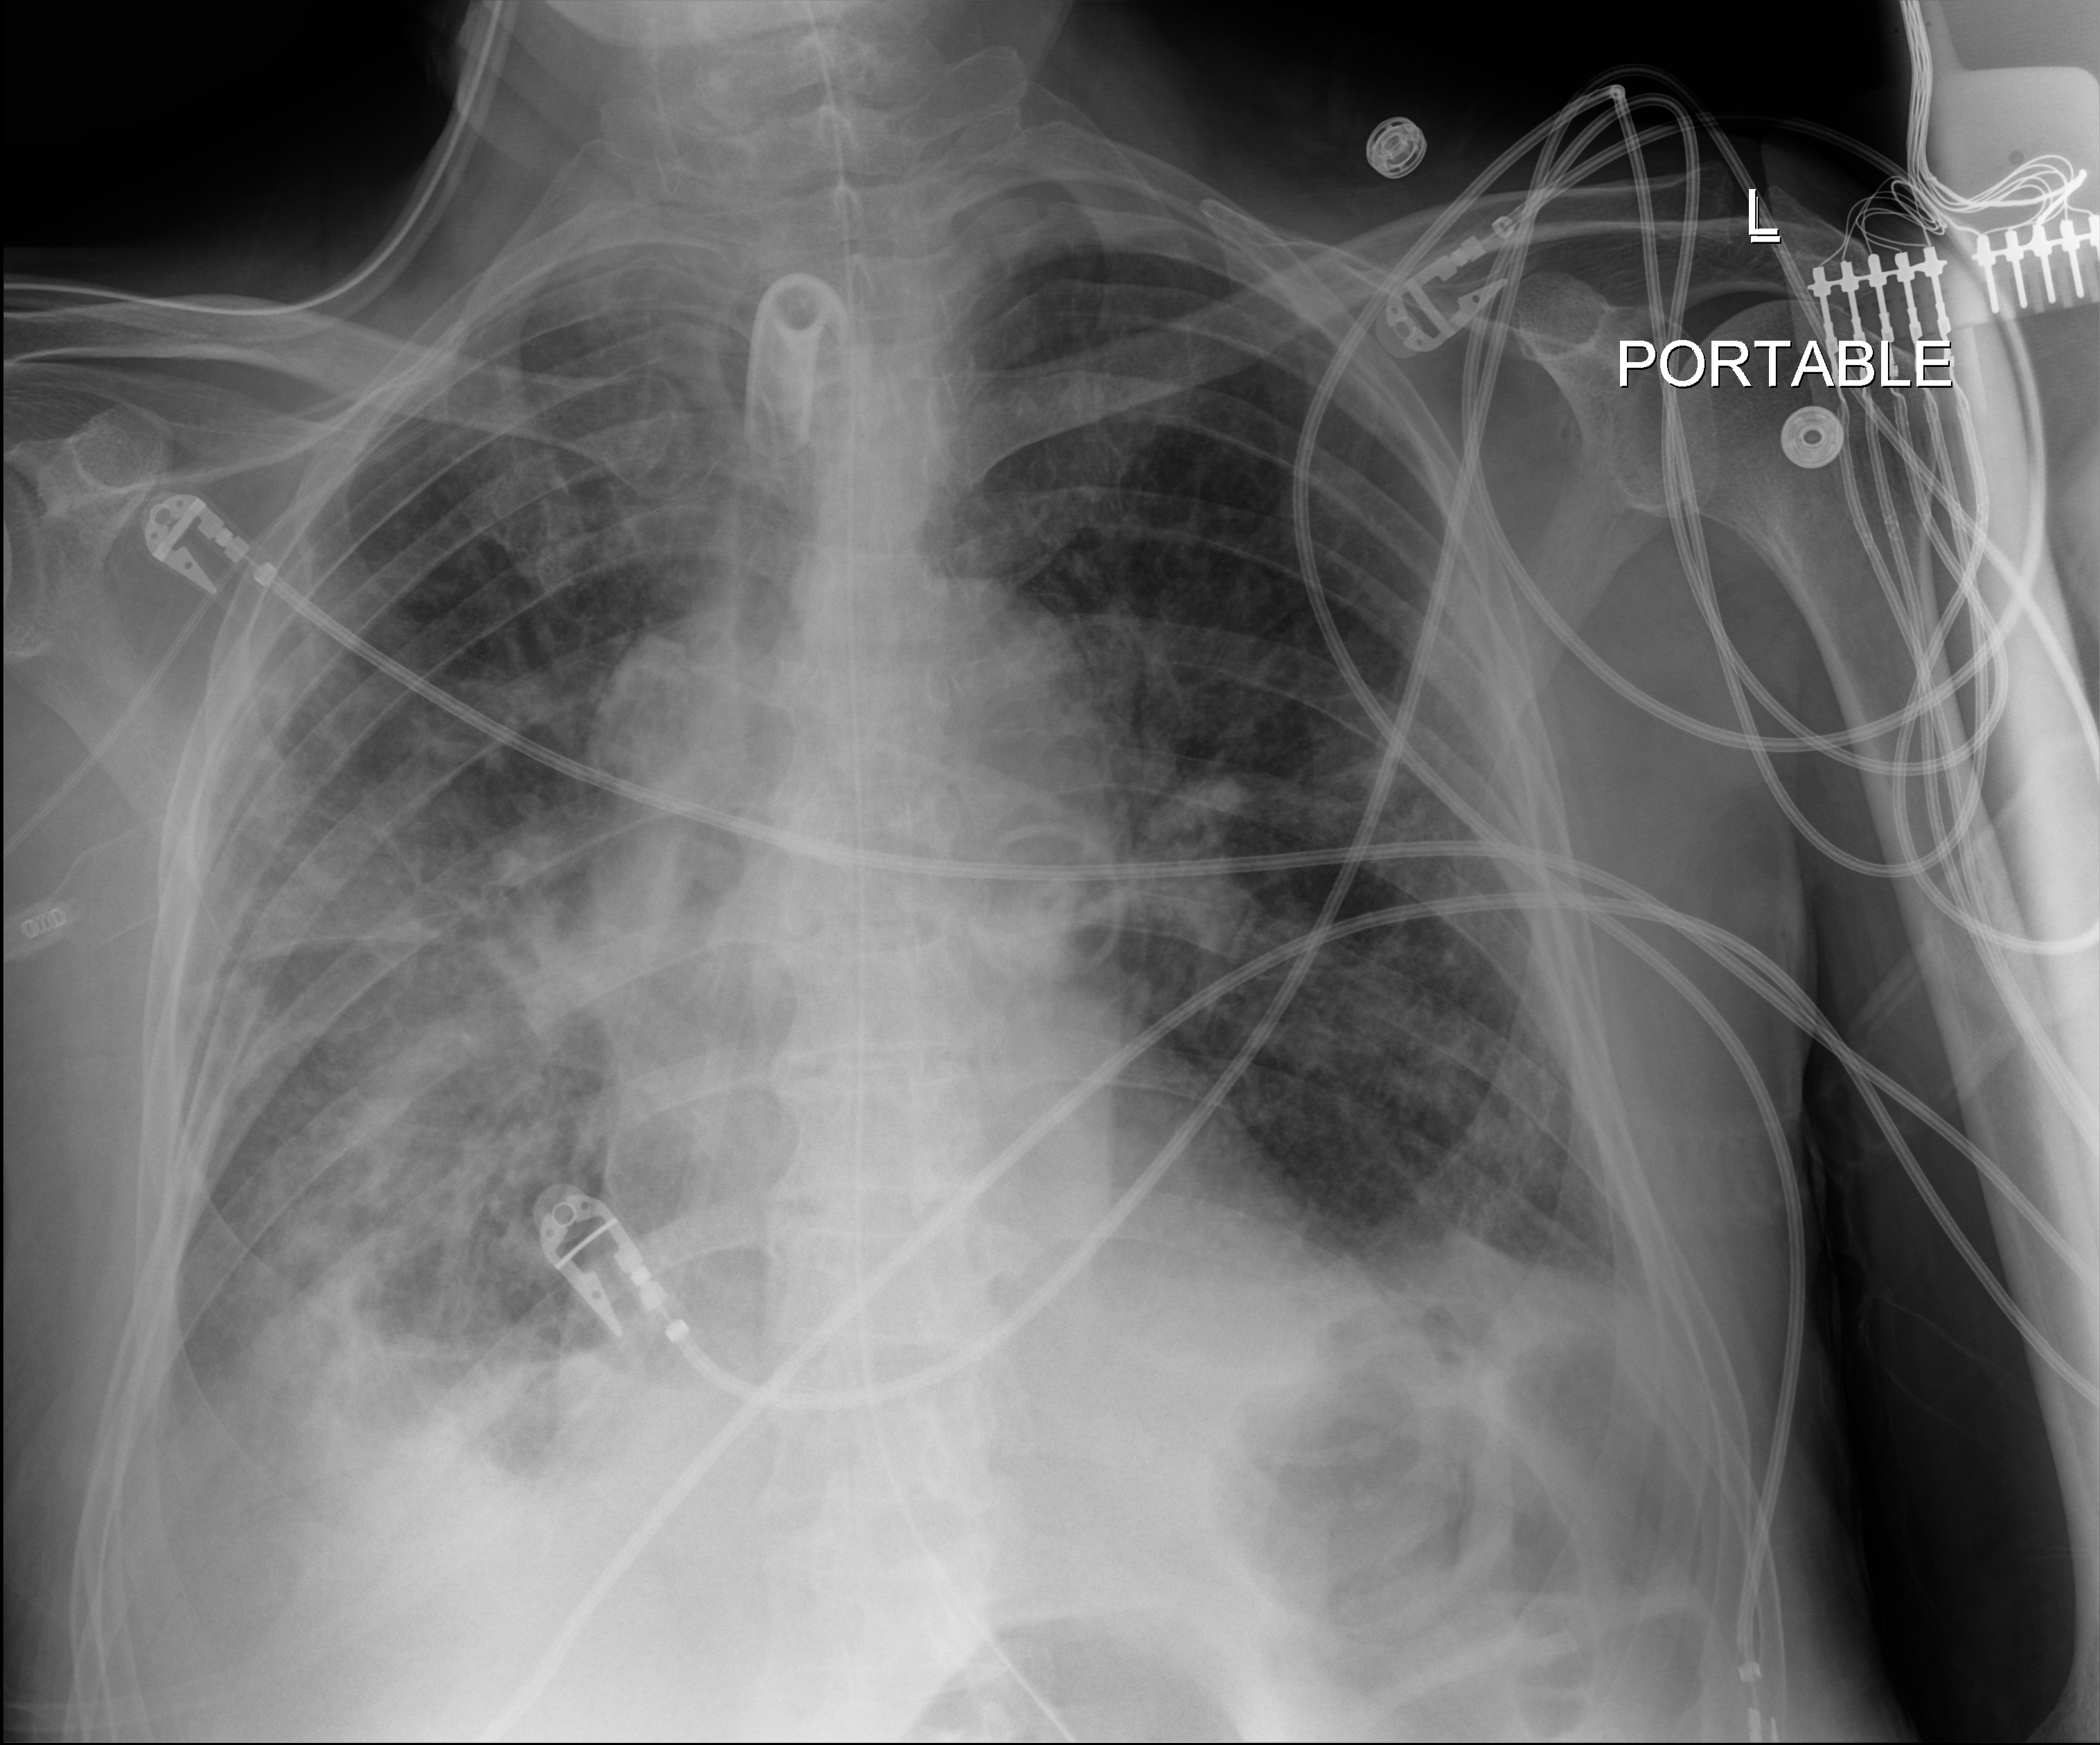
Portable chest radiograph; anteroposterior (AP) projection. Male patient hospitalised with COVID-19, age 75–90 years.
From the hospital-stay record, not from the radiograph (when in the stay this image was taken is not recorded):
- chronic kidney disease (admission record): no